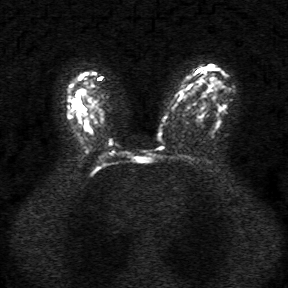
Breast MRI, one axial slice; slice 22 of 34 in the series (ordered by position); diffusion-weighted series; image 2 of 4 stored at this slice position (different b-values; order by instance number); 1.5 T; 5 mm slice thickness; 288 × 288 image matrix. Female patient.
Structures marked on this image (outlined manually by an expert reader):
- tumour on diffusion-weighted imaging: bounding box (x1, y1, x2, y2) in pixels: (74, 102, 78, 107)